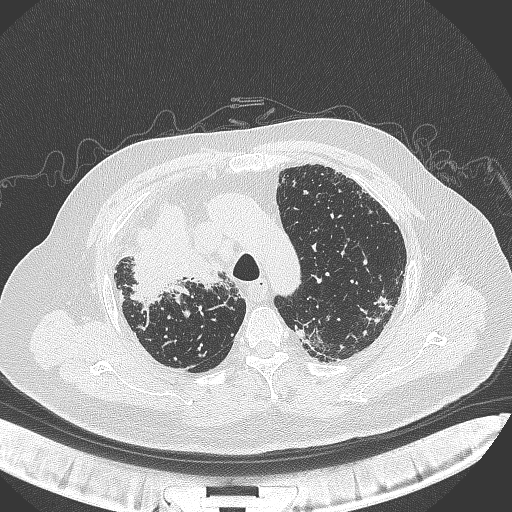
Chest CT, one axial slice; position 271 of 384 along the scan axis; reconstruction kernel B70f; 120 kVp; lung window (W 1500 / L -600 HU); 1 mm slice thickness; 512 × 512 image matrix, field of view 400 × 400 mm. Male patient, age 69 years. Case-level facts recorded for this patient, not image findings: clinical TNM (as recorded): T4 N3 M1.
Outlined on this slice (rectangle marked by the reading radiologist):
- lung tumour (recorded histology: adenocarcinoma): bounding box <127,196,228,304> (left, top, right, bottom; pixels)